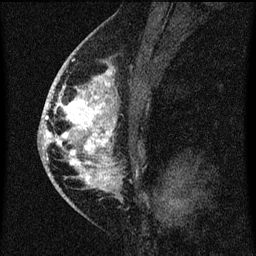
Breast MRI (dynamic contrast-enhanced), one sagittal slice; position 38 of 60 along the scan axis; dynamic contrast-enhanced series, image 2 of 3 at this slice position (ordered by acquisition); 1.5 T; TE 4.2 ms, TR 8 ms; 2 mm slice thickness; 256 × 256 image matrix, field of view 180 × 180 mm. Female patient, age 46 years.
Structures marked on this image (semi-automatically segmented with operator editing):
- analysis volume of interest (the breast-tissue region the enhancement analysis was run in; not a lesion): bounding box <49,68,118,195> (left, top, right, bottom; pixels)
- tumour enhancement mask (voxels above the 70 % enhancement threshold inside the analysis volume of interest): <49,68,117,193>